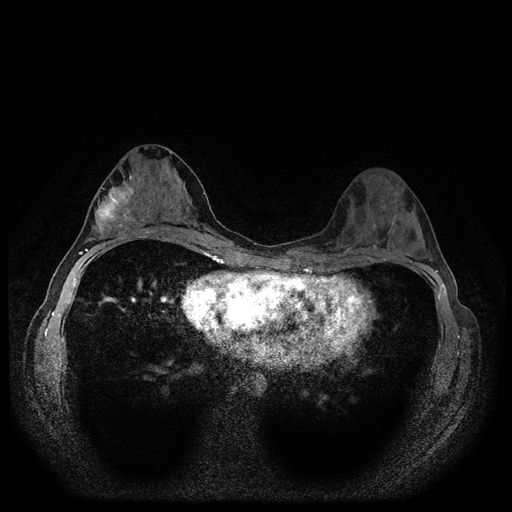
Breast MRI (dynamic contrast-enhanced, multi-phase), one axial slice. Slice 54 of 116 in the series (ordered by position). Dynamic contrast-enhanced series, time point 2 of 5 at this slice position (early post-contrast). 1.5 T. TE 2.7 ms, TR 5.4 ms. 2 mm slice thickness. 512 × 512 image matrix, field of view 320 × 320 mm. Patient: female, 29 years.
Structures marked on this image (semi-automatic segmentation, software-assisted and operator-edited):
- breast lesion (labelled 'tumour' in the annotation; benign lesions carry a separate 'benign' label): bounding box (x1, y1, x2, y2) in pixels: (93, 180, 136, 234)